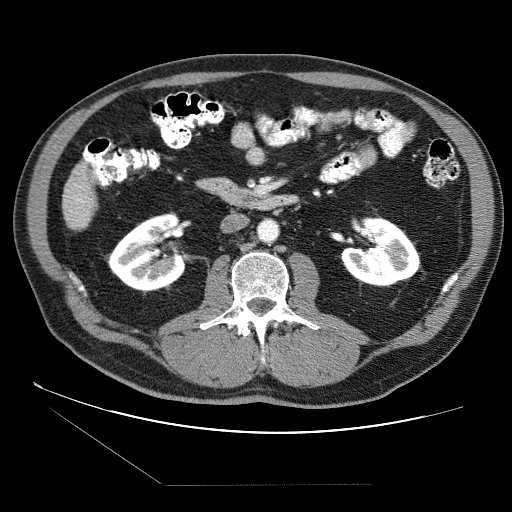
Contrast-enhanced abdominal CT (liver protocol), one axial slice; slice 8 of 87 in the series (ordered by position); soft-tissue window (W 400 / L 40 HU); 2.5 mm slice thickness; 512 × 512 image matrix, field of view 400 × 400 mm. From the clinical record (not read from this slice): diagnosis: hepatocellular carcinoma (patient treated with transarterial chemoembolisation; whether this scan precedes or follows treatment is not stated here); TNM stage (as recorded): Stage-II; Child-Pugh class: B; tumour differentiation: no biopsy; tumour nodularity: multinodular.
Structures marked on this image (semi-automatic segmentation, software-assisted and operator-edited):
- liver parenchyma outside the tumour (the mass and vessels are separate outlines, so this box may not span the whole liver): bounding box [x1, y1, x2, y2] px = [62, 164, 96, 228]
- liver vessels: [75, 184, 84, 203]